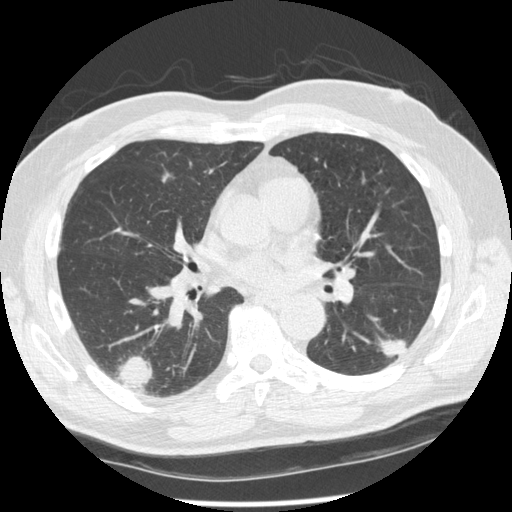
Axial slice from a low-dose chest CT screening exam. Second annual screen. Lung window (W 1500 / L -600 HU). 1.25 mm slice thickness. 120 kVp. 512 × 512 image matrix, field of view 360 × 360 mm. Male participant, aged 74 years at enrolment. Former smoker at enrolment.
Lesion marked by an expert reader, bounding box <367,313,423,368> (left, top, right, bottom; pixels). The screening reader recorded 7 non-calcified nodules or masses ≥4 mm on this exam (right upper lobe, right lower lobe, right upper lobe, right lower lobe, left lower lobe, left upper lobe, left upper lobe); which of them this box marks is not recorded. Official screen result: positive, other. Participant outcome: lung cancer diagnosed 43 days after this screen — squamous cell carcinoma, NOS, left lower lobe, well differentiated (G1), stage IA (AJCC 6th edition), 28 mm at pathology.